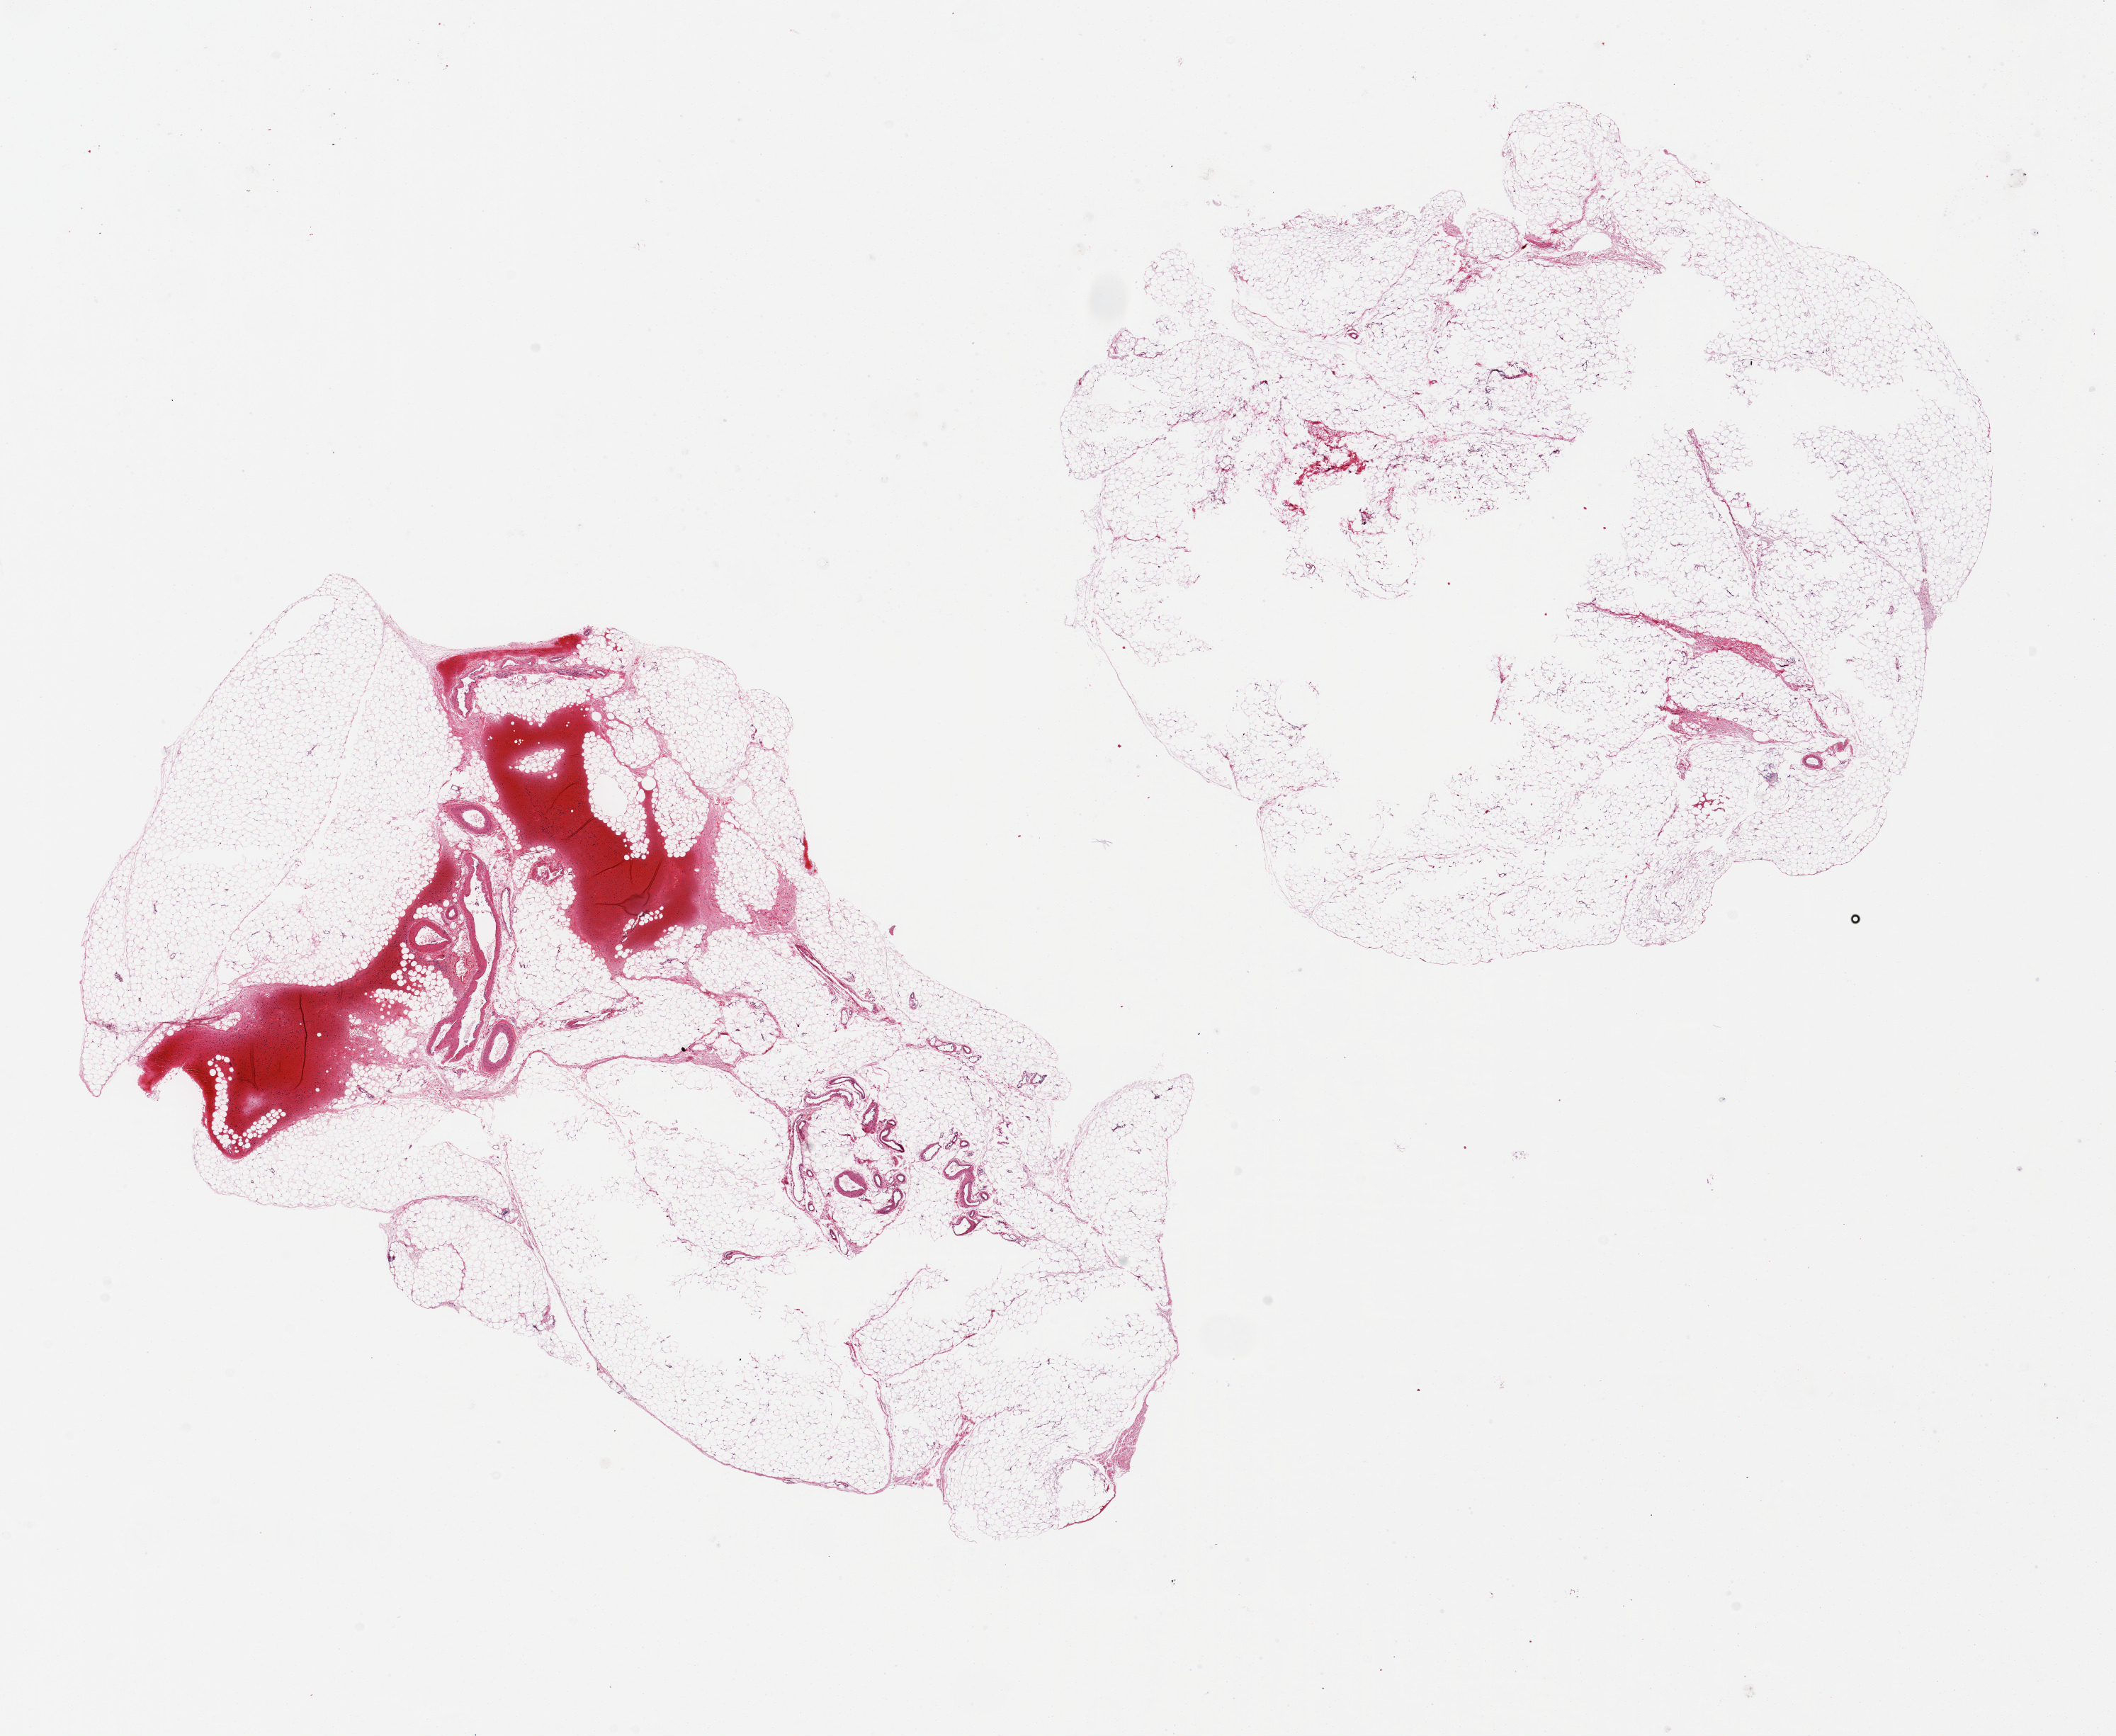
Haematoxylin and eosin whole-slide image, brightfield — shown as a low-resolution overview of the whole scanned area (about 23.6 x 19.4 mm, from a 20x scan), PAXgene-fixed, paraffin-embedded tissue, section of omentum (target tissue), tissue donor sample. Male donor.
• reviewer comment on this tissue sample: 2 pieces ~12x88mm